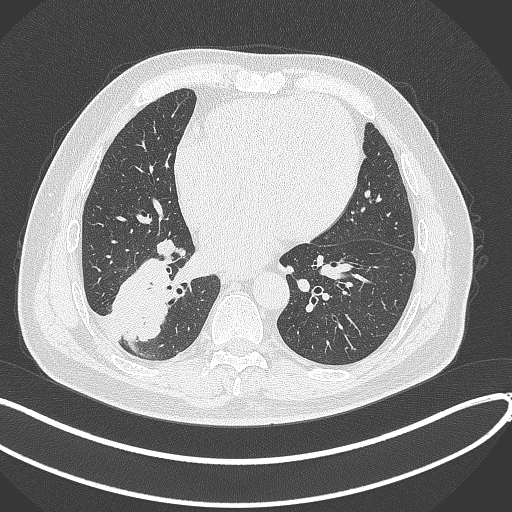
Chest CT, one axial slice; slice 138 of 360 in the series (ordered by position); reconstruction kernel B70f; lung window (W 1500 / L -600 HU); 512 × 512 image matrix. Patient: male, 59 years.
Annotated regions visible in this slice (bounding box drawn by a radiologist):
- lung tumour (recorded histology: adenocarcinoma): bounding box (x1, y1, x2, y2) in pixels: (111, 253, 173, 343)